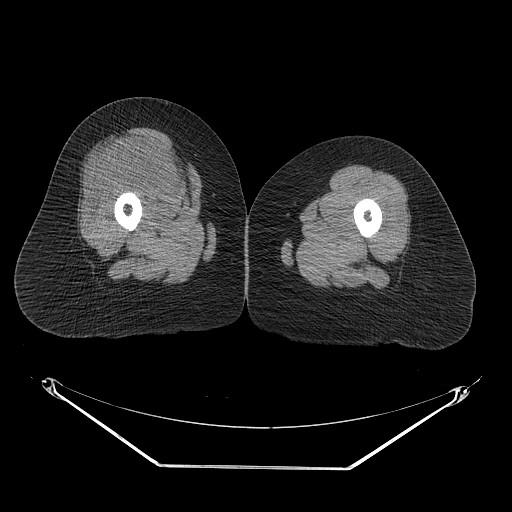
CT of an extremity soft-tissue mass (from a PET/CT study), one axial slice. Slice 28 of 267 in the series (ordered by position). Reconstruction kernel STANDARD. Soft-tissue window (W 400 / L 40 HU). 3.75 mm slice thickness. 512 × 512 image matrix, field of view 500 × 500 mm. Female patient. From the clinical record (not read from this slice): histological type: malignant solitary fibrous tumor; grade: intermediate; site of the primary tumour: right thigh.
Outlined on this slice (expert contour drawn on MRI and transferred to this co-registered scan by the dataset authors):
- gross tumour volume including surrounding oedema: box from (x=100, y=132) to (x=202, y=216) px
- gross tumour volume (mass): (x=103, y=133)–(x=197, y=207)